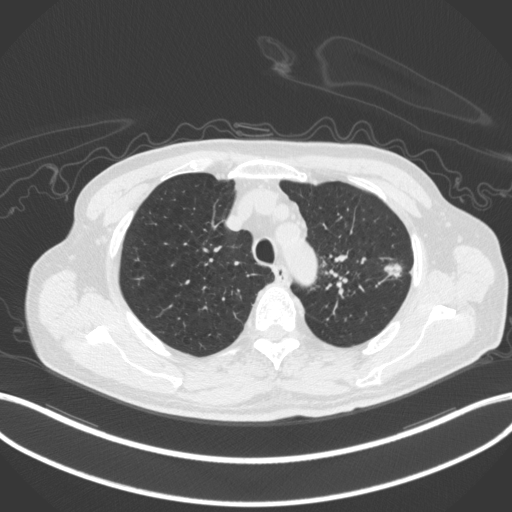
Chest CT, one axial slice; slice 349 of 420 in the series (ordered by position); lung window (W 1500 / L -600 HU); 1 mm slice thickness; 512 × 512 image matrix, field of view 400 × 400 mm. Male patient, age 77 years. From the clinical record (not read from this slice): clinical TNM (as recorded): T3 N1 M0.
Structures marked on this image (bounding box drawn by a radiologist):
- lung tumour (recorded histology: adenocarcinoma): bounding box (x1, y1, x2, y2) in pixels: (382, 260, 405, 279)